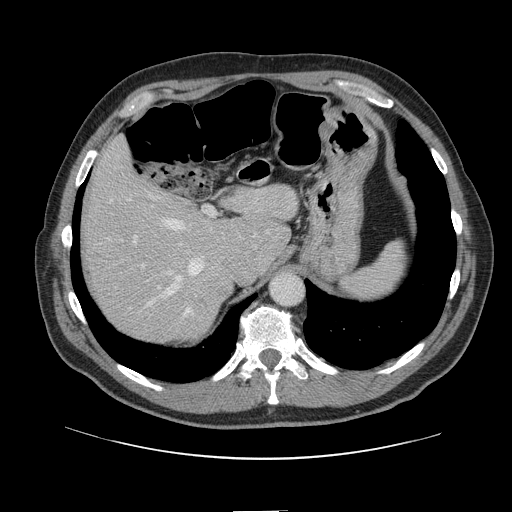
Contrast-enhanced abdominal CT, one axial slice. Position 104 of 161 along the scan axis. 120 kVp. Intravenous contrast given. Soft-tissue window (W 400 / L 40 HU). 512 × 512 image matrix, field of view 412 × 412 mm. Male patient, age 66 years. From the clinical record (not read from this slice): diagnosis: colorectal cancer liver metastases, imaged before liver resection; multiple liver metastases: no.
Structures marked on this image (outlined manually by an expert reader):
- hepatic veins: bounding box <110,167,205,313> (left, top, right, bottom; pixels)
- liver: <84,143,297,342>
- planned liver remnant (the part of the liver to remain after resection): <84,143,297,308>
- portal vein (with intrahepatic branches): <129,206,216,309>
- liver metastasis: <193,292,210,315>